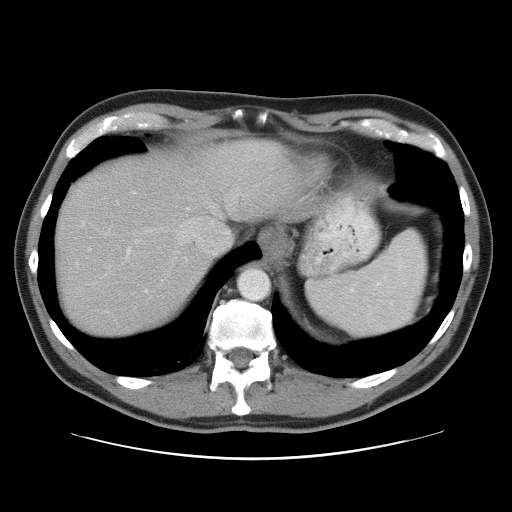
Contrast-enhanced abdominal CT, one axial slice; slice 45 of 52 in the series (ordered by position); reconstruction kernel STANDARD; intravenous contrast given; soft-tissue window (W 400 / L 40 HU); 5 mm slice thickness; 512 × 512 image matrix, field of view 393 × 393 mm. Male patient, age 70 years. From the clinical record (not read from this slice): diagnosis: colorectal cancer liver metastases, imaged before liver resection; multiple liver metastases: yes; largest metastasis: 4 cm; disease in both lobes: yes.
Annotated regions visible in this slice (expert manual segmentation):
- hepatic veins: bounding box [x1, y1, x2, y2] px = [144, 189, 244, 293]
- liver: [55, 141, 298, 340]
- planned liver remnant (the part of the liver to remain after resection): [132, 141, 298, 219]